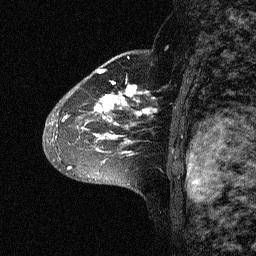
Breast MRI (dynamic contrast-enhanced), one sagittal slice. Slice 43 of 64 in the series (ordered by position). Dynamic contrast-enhanced study with each time point stored as its own series, time point 2 of 3 at this slice position (early post-contrast, ordered by acquisition time). 1.5 T. TE 4.5 ms, TR 11 ms. 2.06 mm slice thickness. 256 × 256 image matrix, field of view 200 × 200 mm. Patient: female, 46 years. Case-level facts recorded for this patient, not image findings: setting: breast cancer imaged before/during neoadjuvant chemotherapy; receptor status: HER2-positive.
Annotated regions visible in this slice (semi-automatic segmentation, software-assisted and operator-edited):
- analysis volume of interest (the breast-tissue region the enhancement analysis was run in; not a lesion): bounding box (x1, y1, x2, y2) in pixels: (43, 72, 164, 177)
- tumour enhancement mask (voxels above the 90 % enhancement threshold inside the analysis volume of interest): (68, 72, 158, 169)